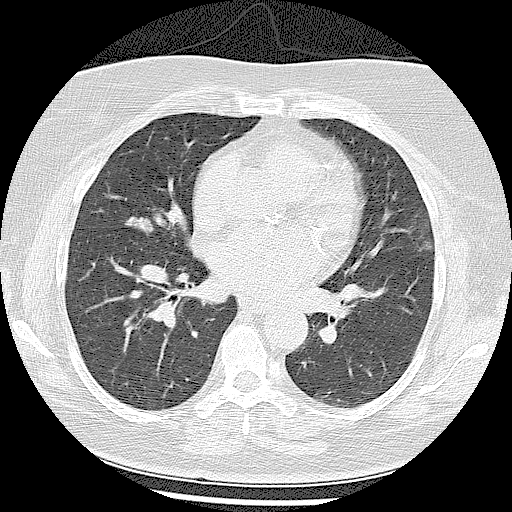
Low-dose screening chest CT, axial slice. First (baseline) screen. Lung window (W 1500 / L -600 HU). 2.5 mm slice thickness. Lung (sharp) reconstruction kernel (LUNG). 512 × 512 image matrix. Female, age 57 years at enrolment. Former smoker at enrolment.
Expert-annotated lung lesion, bounding box (x1, y1, x2, y2) in pixels: (104, 197, 168, 252). The screening reader recorded 4 non-calcified nodules or masses ≥4 mm on this exam; which of them this box marks is not recorded. Official screen result: positive, change unspecified: nodule(s) >= 4 mm or enlarging nodule(s), mass(es), or other non-specific abnormalities suspicious for lung cancer. Participant outcome: lung cancer diagnosed 87 days after this screen — adenocarcinoma, NOS, right middle lobe, well differentiated (G1), stage IA (AJCC 6th edition), 21 mm at pathology.